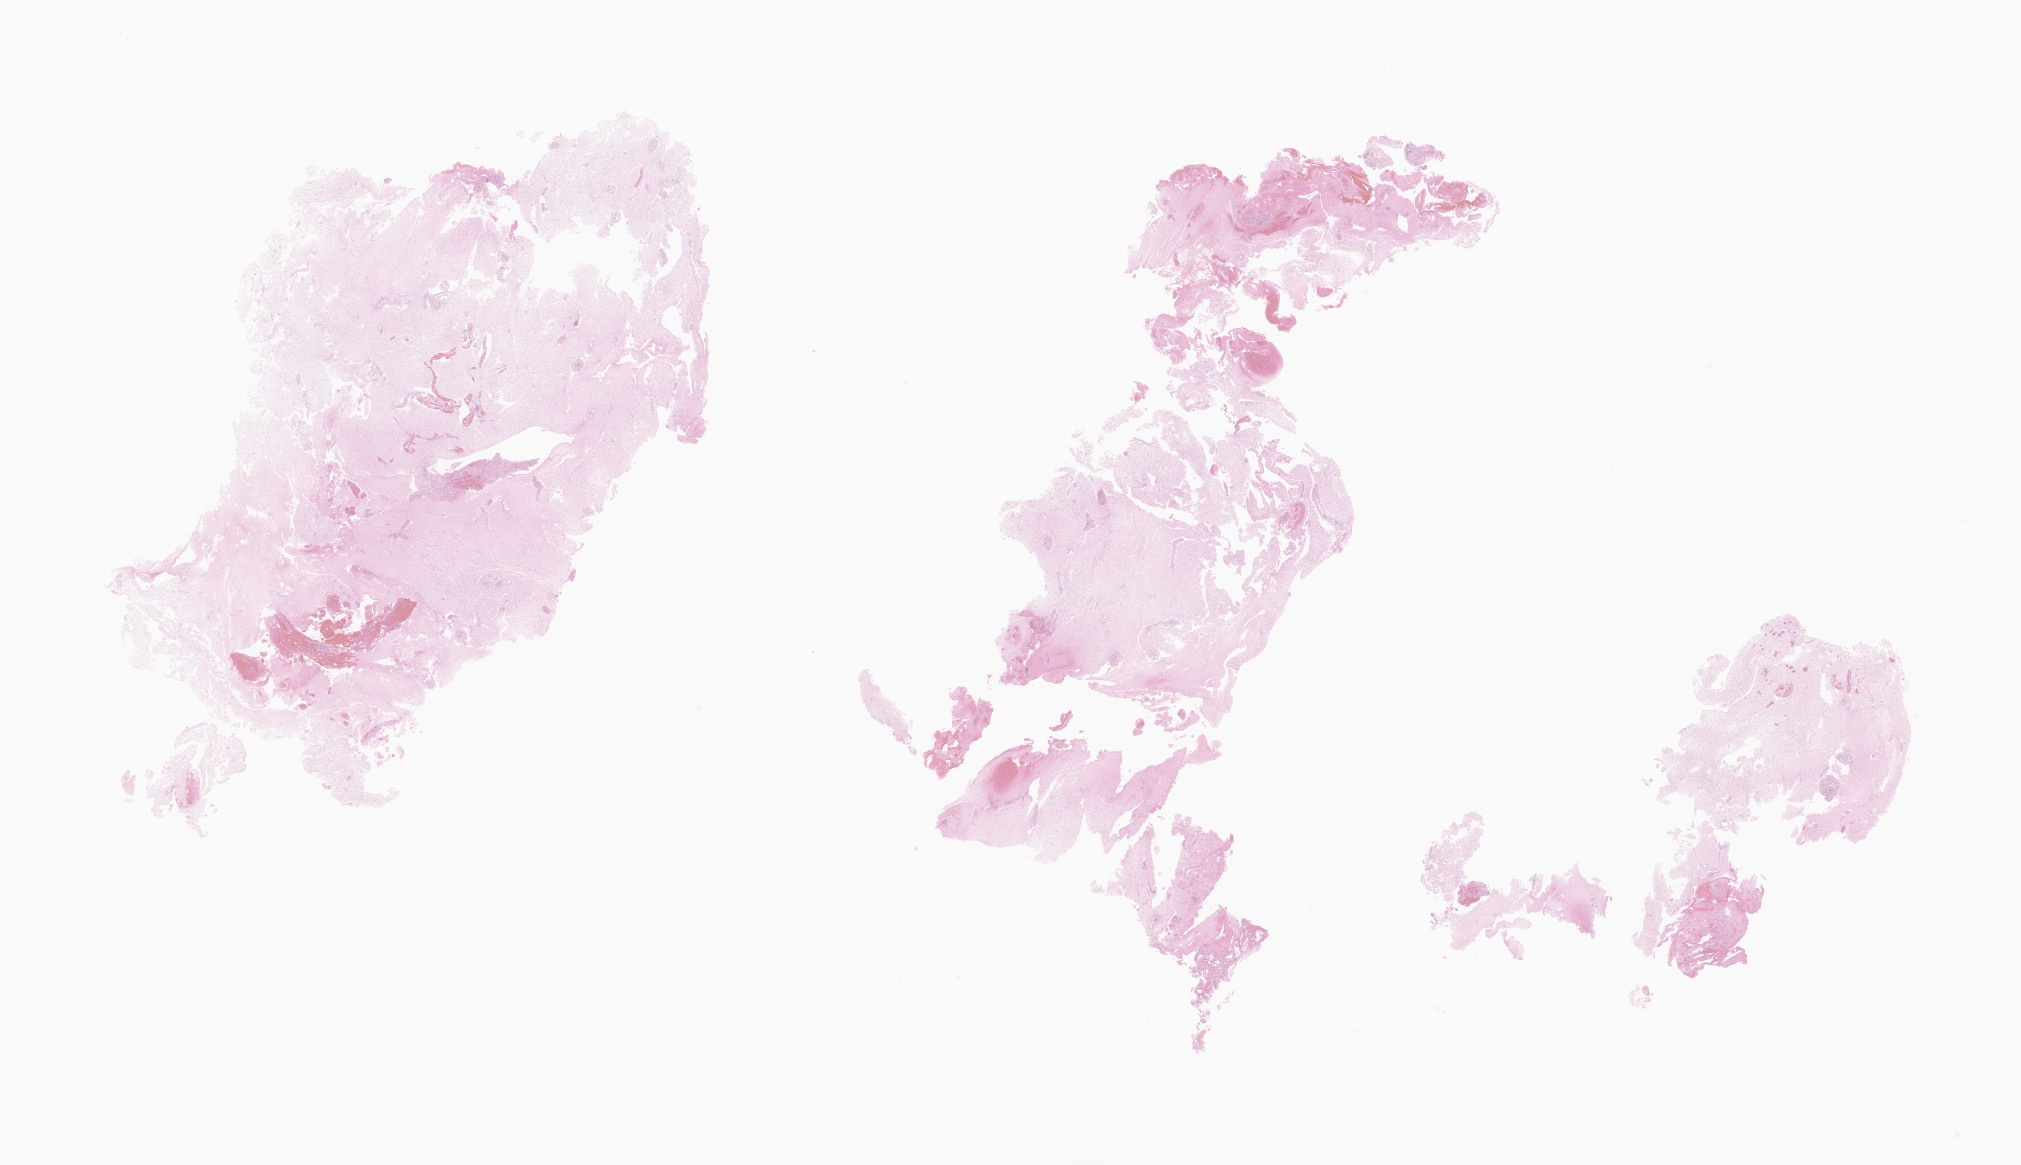
Whole-slide image, hematoxylin and eosin (H&E) stain of tumor tissue from the brain, shown as a low-resolution overview of the whole scanned area (about 34.1 x 19.6 mm), formalin-fixed, paraffin-embedded (FFPE) tissue. Patient: male, age 97 months (8 years 1 month).
Diagnosis (ICD-O-3 morphology term): Pilocytic astrocytoma.